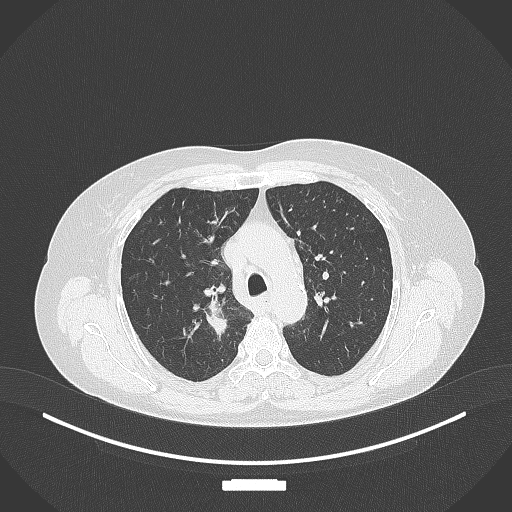
Chest CT, one axial slice. Position 270 of 357 along the scan axis. 120 kVp. Lung window (W 1500 / L -600 HU). 512 × 512 image matrix. Female patient, age 62 years. Case-level facts recorded for this patient, not image findings: clinical TNM (as recorded): T1c N1 M0.
Outlined on this slice (rectangle marked by the reading radiologist):
- lung tumour (recorded histology: squamous cell carcinoma): box from (x=201, y=300) to (x=232, y=337) px